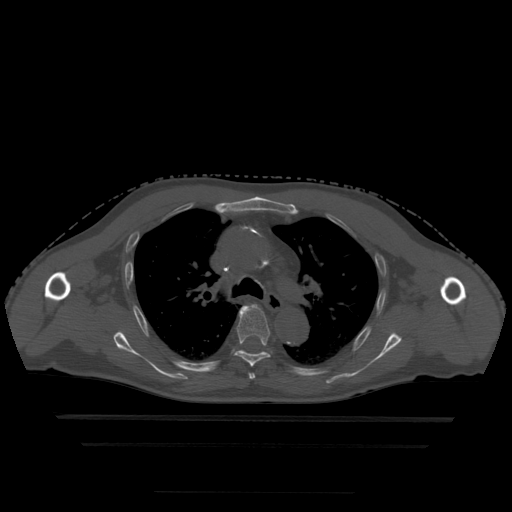
CT including the spine, one axial slice. Bone window (W 1800 / L 400 HU). 1.25 mm slice thickness. 512 × 512 image matrix, field of view 436 × 436 mm. Patient age 68 years. Case-level facts recorded for this patient, not image findings: primary cancer: urothelial.
Outlined on this slice (semi-automatic segmentation, software-assisted and operator-edited):
- T4 vertebra: box from (x=249, y=373) to (x=255, y=380) px
- T5 vertebra: (x=235, y=306)–(x=270, y=367)